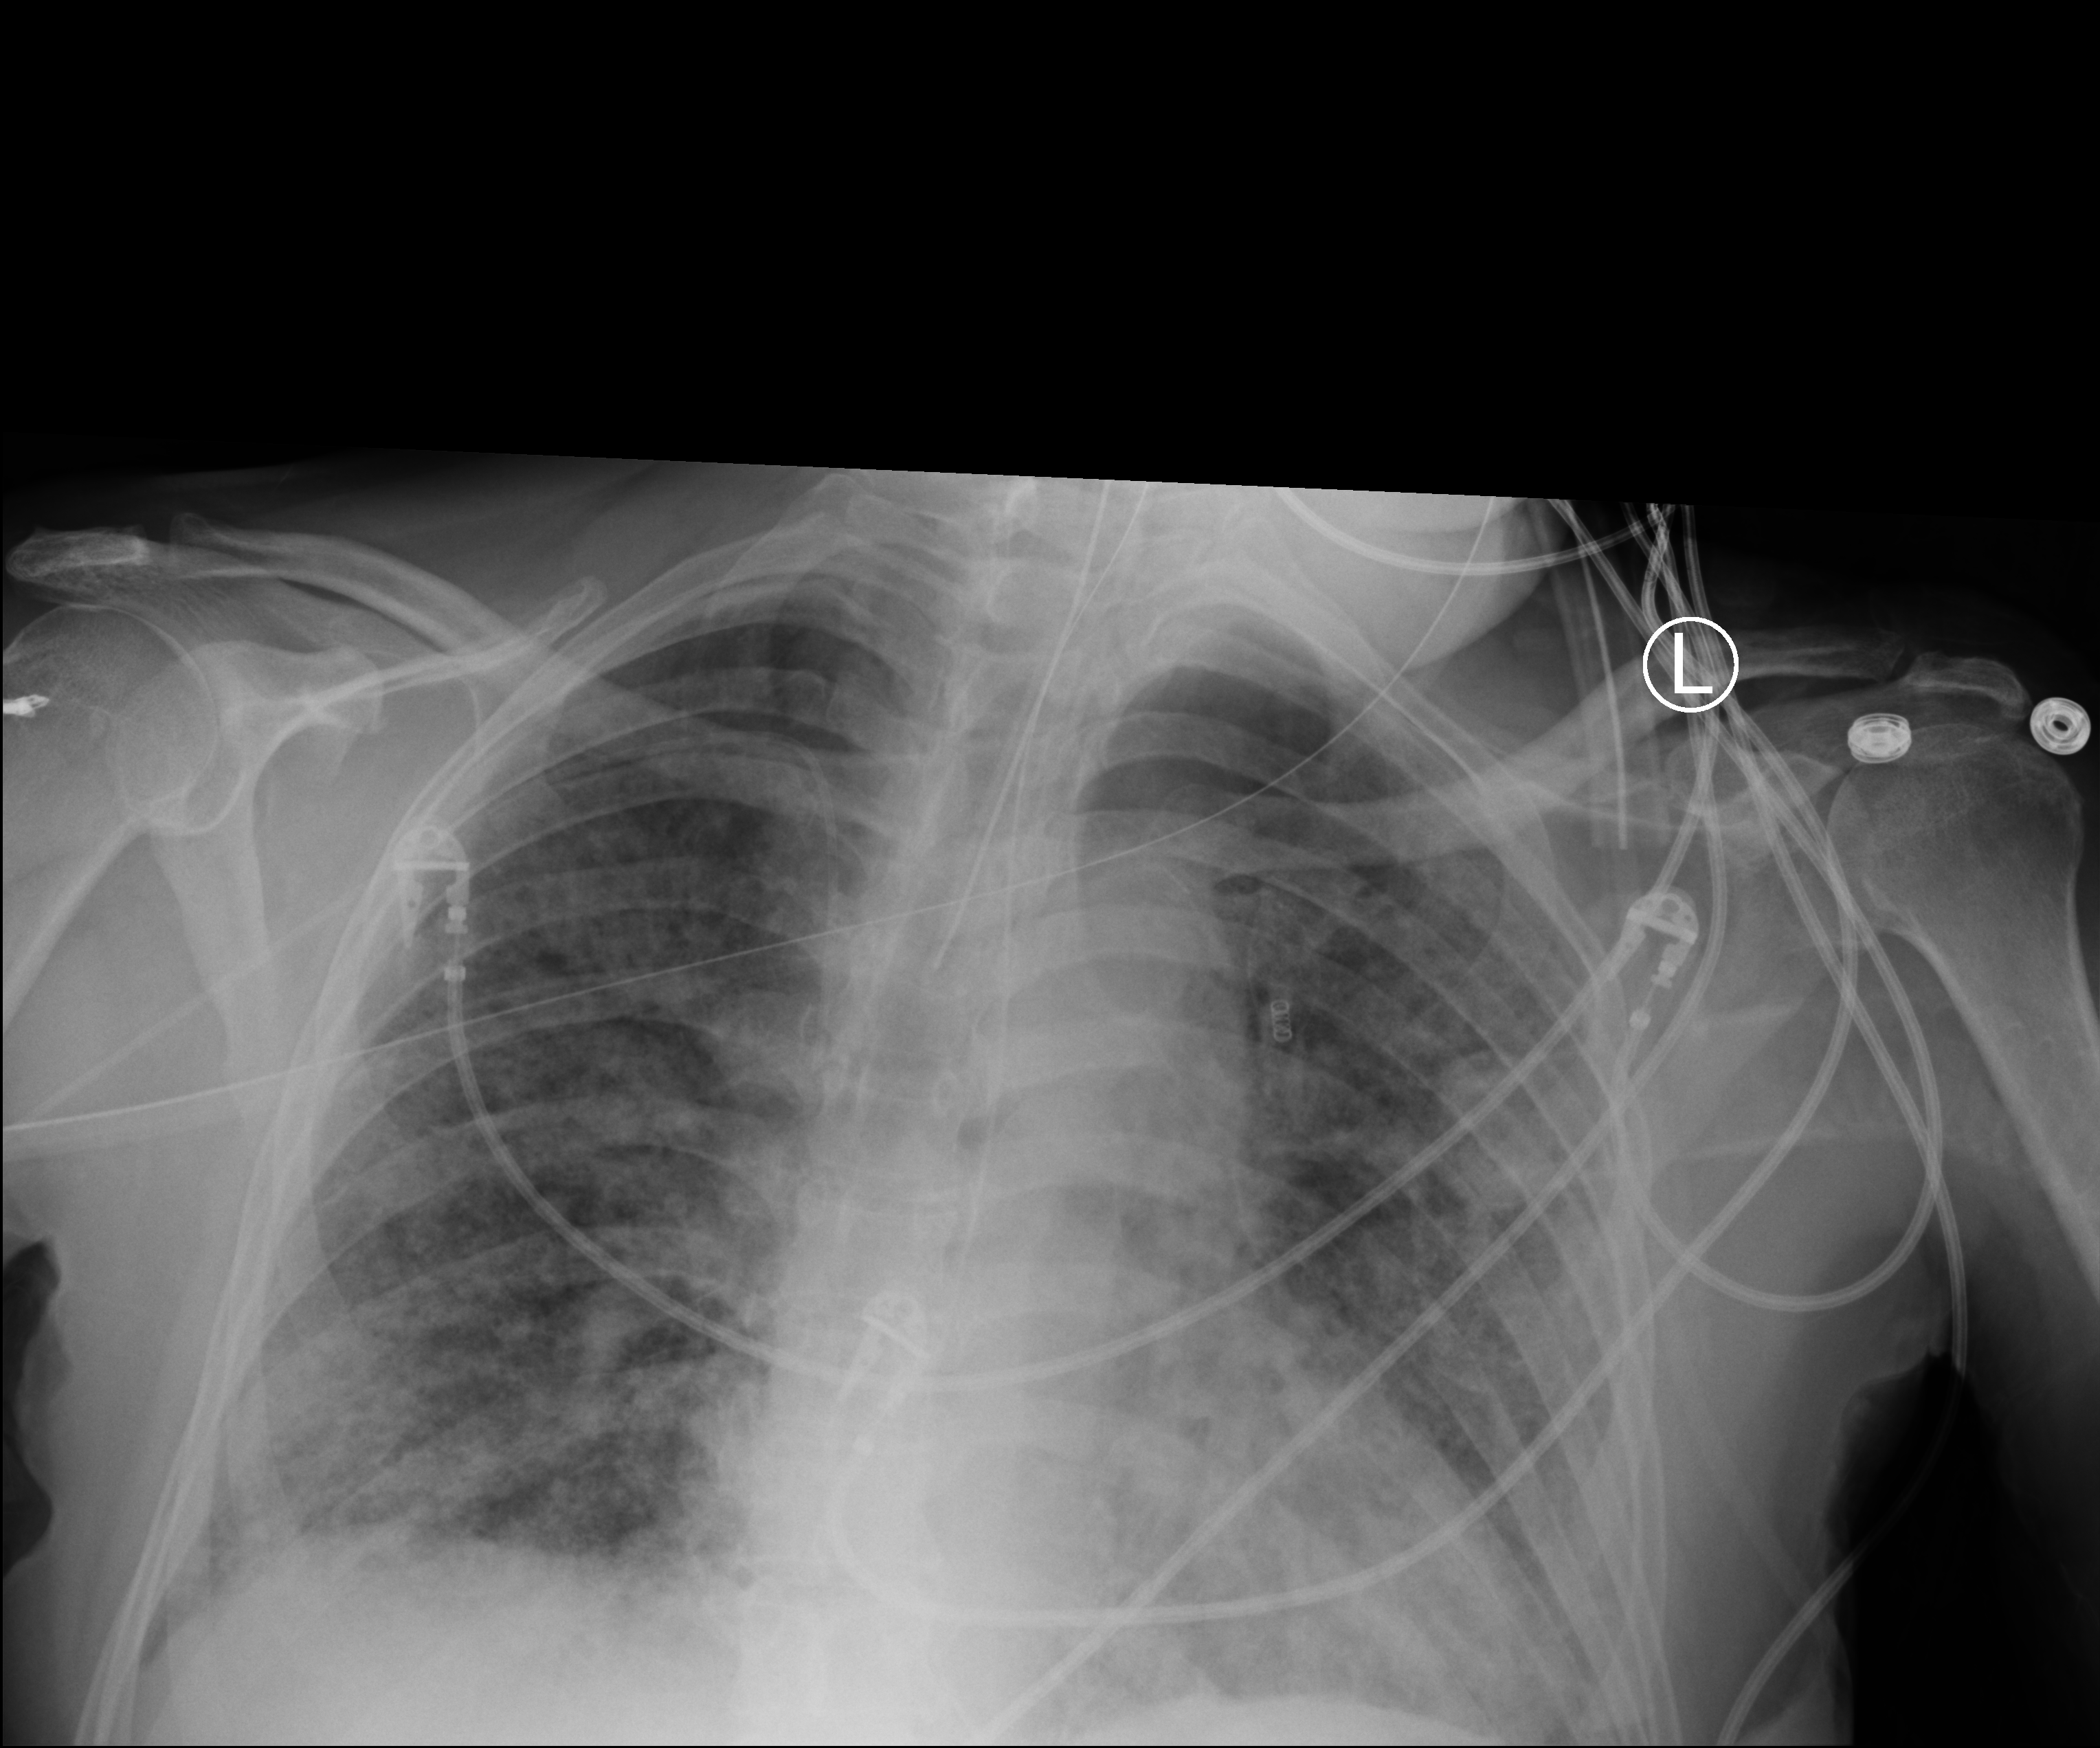
Portable chest radiograph, anteroposterior (AP) projection. Male patient hospitalised with COVID-19, age 60–74 years.
Hospital-stay facts (about this admission, not read from this image; timing relative to this image not recorded): mechanically ventilated during this hospital stay: yes.